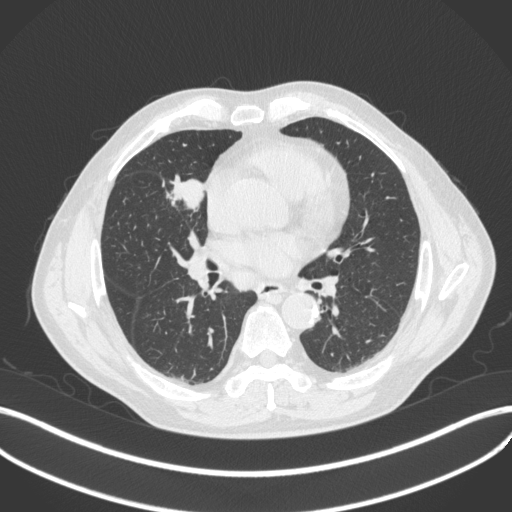
Chest CT, one axial slice. Slice 200 of 429 in the series (ordered by position). Reconstruction kernel B31f. Lung window (W 1500 / L -600 HU). 1 mm slice thickness. 512 × 512 image matrix, field of view 400 × 400 mm. Patient: male, 61 years. Case-level facts recorded for this patient, not image findings: clinical TNM (as recorded): T2b N1 M0.
Outlined on this slice (rectangle marked by the reading radiologist):
- lung tumour (recorded histology: squamous cell carcinoma): box from (x=165, y=175) to (x=208, y=217) px